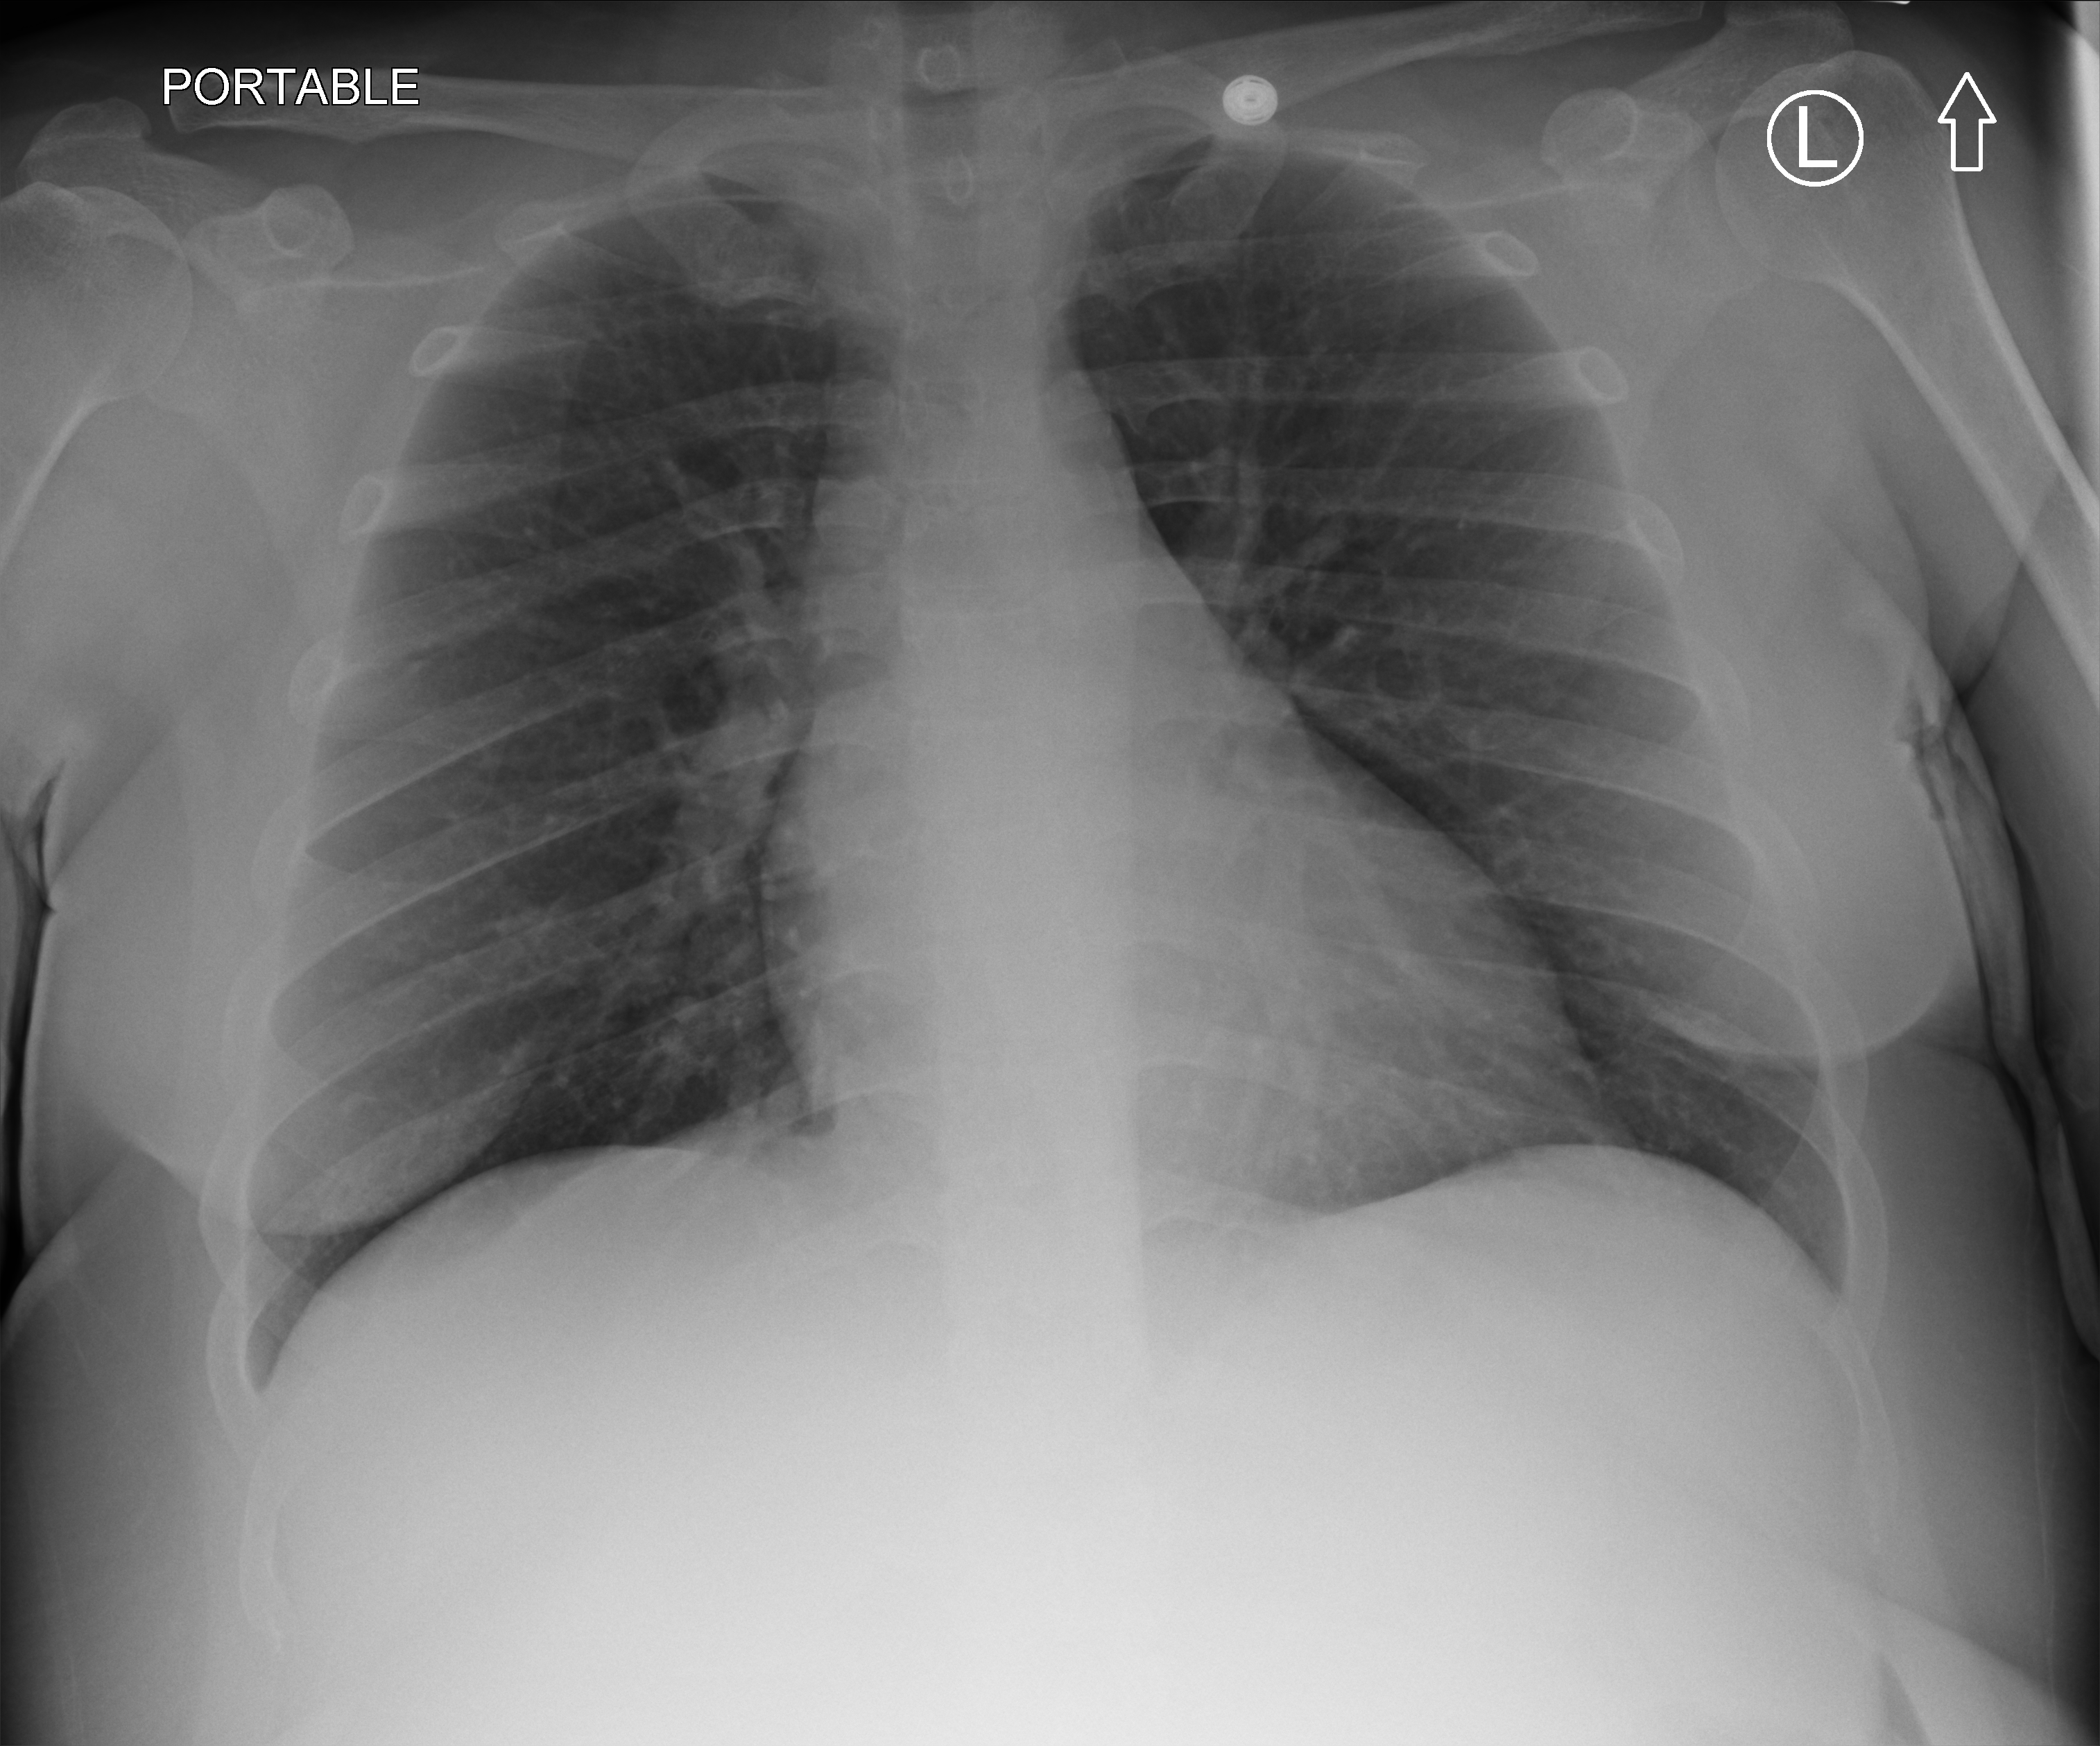
Chest X-ray (portable); anteroposterior (AP) projection. Female patient hospitalised with COVID-19, age 18–59 years.
Hospital-stay facts (about this admission, not read from this image; timing relative to this image not recorded): admitted to intensive care during this hospital stay: no.